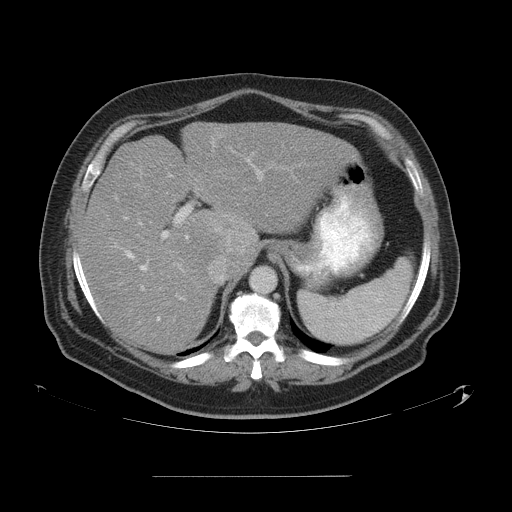
Contrast-enhanced abdominal CT, one axial slice; position 39 of 58 along the scan axis; 120 kVp; intravenous contrast given; soft-tissue window (W 400 / L 40 HU); 5 mm slice thickness; 512 × 512 image matrix. Male patient, age 63 years. From the clinical record (not read from this slice): diagnosis: colorectal cancer liver metastases, imaged before liver resection; multiple liver metastases: no.
Outlined on this slice (outlined manually by an expert reader):
- hepatic veins: bounding box (x1, y1, x2, y2) in pixels: (115, 165, 263, 321)
- liver: (79, 123, 353, 354)
- planned liver remnant (the part of the liver to remain after resection): (79, 195, 216, 354)
- portal vein (with intrahepatic branches): (126, 158, 252, 296)
- liver metastasis: (214, 220, 246, 254)